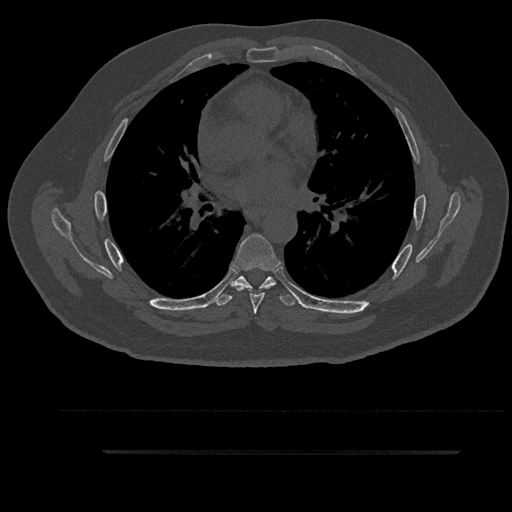
CT including the spine, one axial slice; slice 559 of 797 in the series (ordered by position); 120 kVp; bone window (W 1800 / L 400 HU); 0.5 mm slice thickness; 512 × 512 image matrix, field of view 432 × 432 mm. Male patient, age 63 years. Case-level facts recorded for this patient, not image findings: primary cancer: renal.
Structures marked on this image (semi-automatic segmentation, software-assisted and operator-edited):
- T5 vertebra: bounding box <247,277,271,292> (left, top, right, bottom; pixels)
- T6 vertebra: <231,234,281,314>
- T7 vertebra: <216,276,298,306>